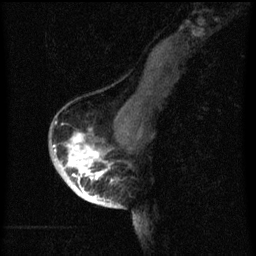
Breast MRI (dynamic contrast-enhanced), one sagittal slice; position 40 of 60 along the scan axis; dynamic contrast-enhanced series, image 2 of 3 at this slice position (ordered by acquisition); 1.5 T; TE 4.2 ms, TR 8 ms; 2 mm slice thickness; 256 × 256 image matrix, field of view 180 × 180 mm. Patient: female, 56 years.
Annotated regions visible in this slice (semi-automatically segmented with operator editing):
- analysis volume of interest (the breast-tissue region the enhancement analysis was run in; not a lesion): box from (x=54, y=122) to (x=120, y=199) px
- tumour enhancement mask (voxels above the 70 % enhancement threshold inside the analysis volume of interest): (x=54, y=134)–(x=113, y=199)